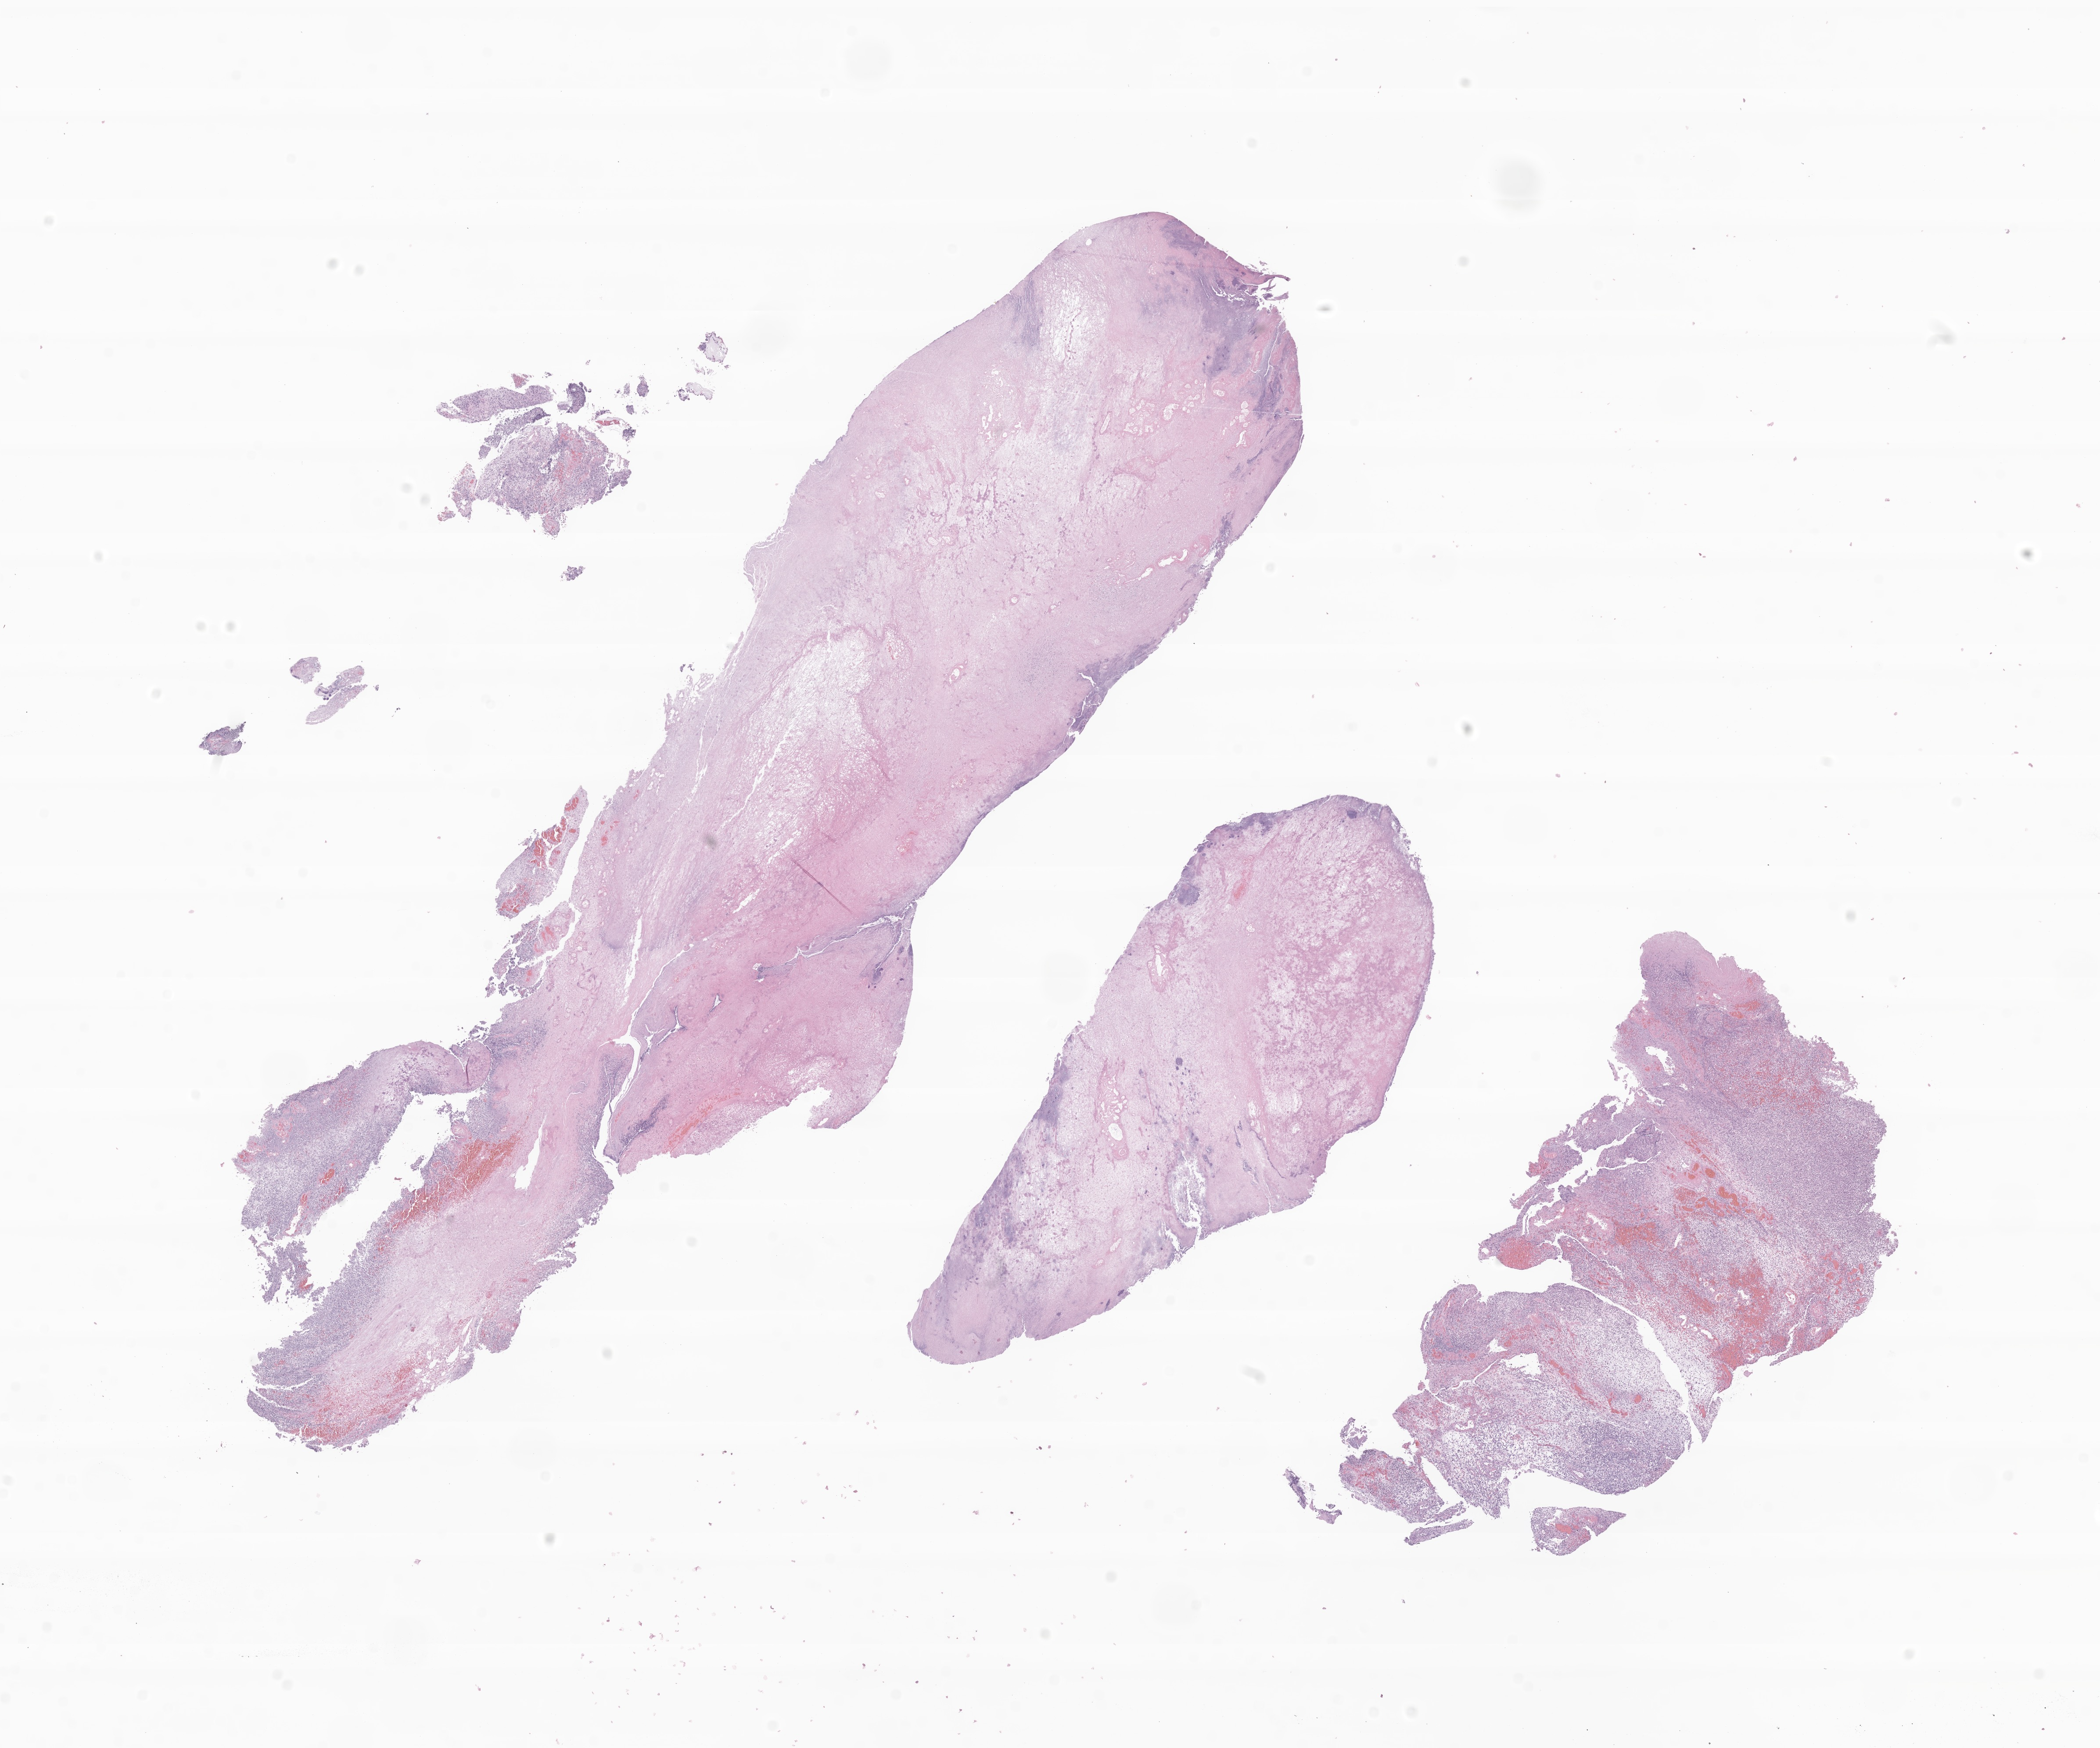
Whole-slide image, haematoxylin and eosin stain of tumor tissue from the nasal cavity — a low-resolution overview of the entire scanned area, about 20.2 x 16.8 mm. Formalin-fixed, paraffin-embedded (FFPE) tissue. Patient: female, age 143 months (11 years 11 months).
Recorded diagnosis: Neoplasm, malignant.